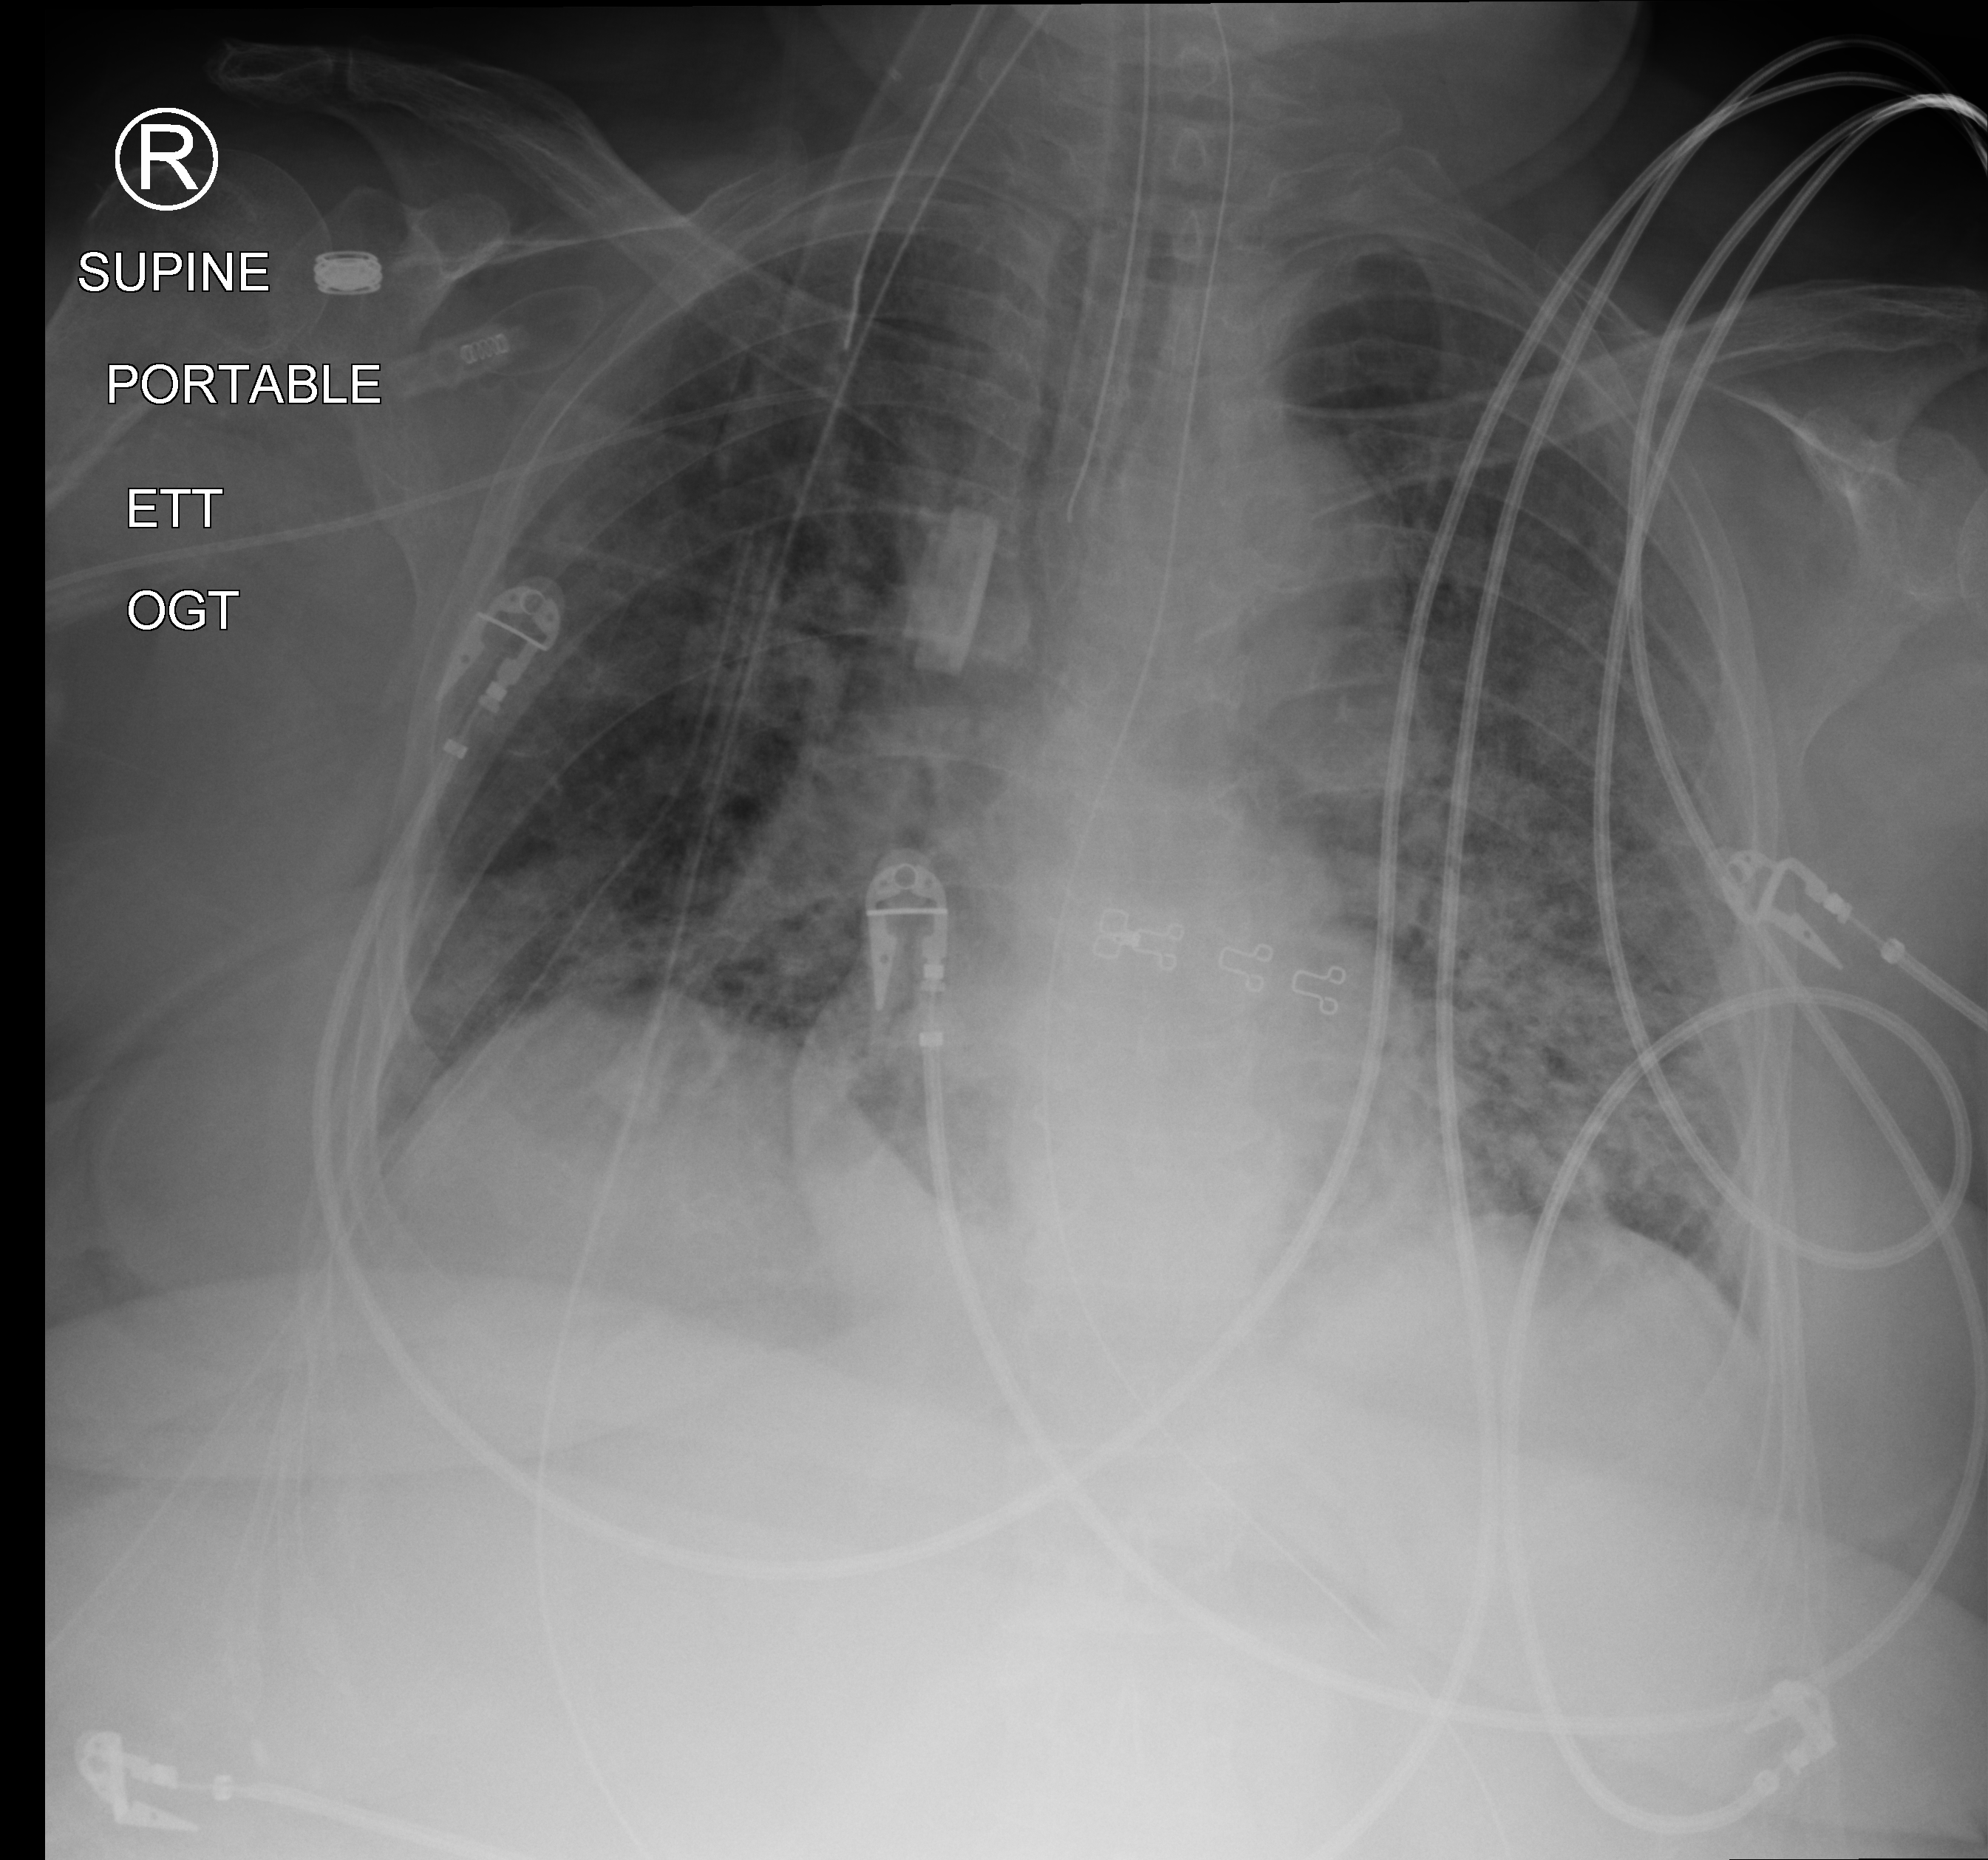
Portable chest radiograph, anteroposterior (AP) projection. Female patient hospitalised with COVID-19, age 60–74 years.
Hospital-stay facts (about this admission, not read from this image; timing relative to this image not recorded):
- hypertension (admission record): yes